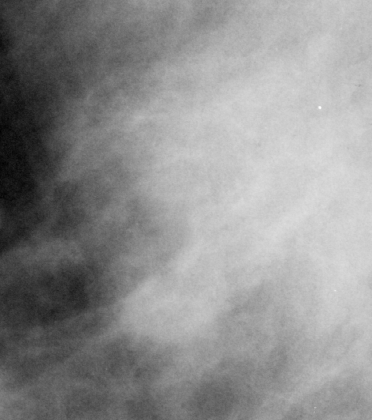
Crop from a digitized film mammogram around one marked abnormality; right breast; MLO view.
Marked abnormality: mass, shape irregular, margins ill defined; BI-RADS assessment category 4; pathology (as recorded): malignant.